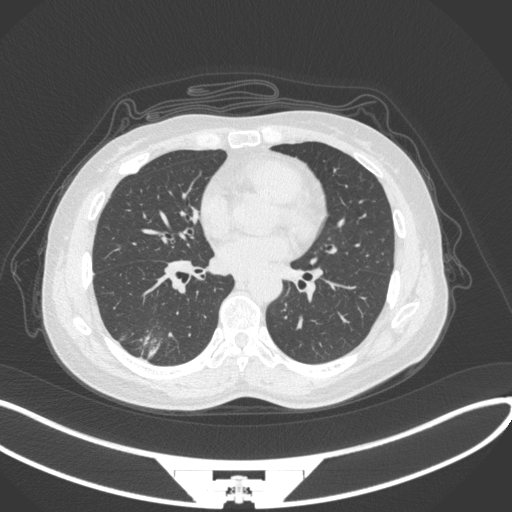
Chest CT, one axial slice; slice 132 of 352 in the series (ordered by position); reconstruction kernel B31f; lung window (W 1500 / L -600 HU); 512 × 512 image matrix. Female patient, age 55 years. Case-level facts recorded for this patient, not image findings: clinical TNM (as recorded): T1c N1 M0.
Structures marked on this image (bounding box drawn by a radiologist):
- lung tumour (recorded histology: adenocarcinoma): bounding box [x1, y1, x2, y2] px = [137, 324, 173, 361]